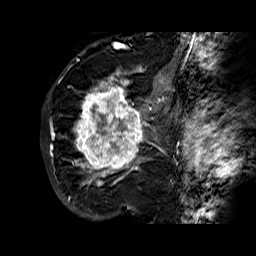
Breast MRI (dynamic contrast-enhanced), one sagittal slice. Dynamic contrast-enhanced series, time point 2 of 6 at this slice position (early post-contrast). 1.5 T. TE 6.3 ms, TR 32.4 ms. 4 mm slice thickness. 256 × 256 image matrix. Female patient. From the clinical record (not read from this slice): setting: breast cancer imaged before/during neoadjuvant chemotherapy; receptor status: HR-positive, HER2-negative.
Outlined on this slice (semi-automatic segmentation, software-assisted and operator-edited):
- analysis volume of interest (the breast-tissue region the enhancement analysis was run in; not a lesion): bounding box (x1, y1, x2, y2) in pixels: (68, 72, 177, 183)
- tumour enhancement mask (voxels above the 100 % enhancement threshold inside the analysis volume of interest): (73, 72, 165, 183)